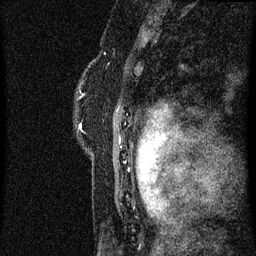
Breast MRI (dynamic contrast-enhanced), one sagittal slice. Position 50 of 60 along the scan axis. Dynamic contrast-enhanced series, image 2 of 3 at this slice position (ordered by acquisition). 1.5 T. TE 4.2 ms, TR 8 ms. 256 × 256 image matrix, field of view 180 × 180 mm. Female patient, age 47 years.
Structures marked on this image (semi-automatically segmented with operator editing):
- analysis volume of interest (the breast-tissue region the enhancement analysis was run in; not a lesion): bounding box <76,80,147,185> (left, top, right, bottom; pixels)
- tumour enhancement mask (voxels above the 70 % enhancement threshold inside the analysis volume of interest): <80,124,147,163>